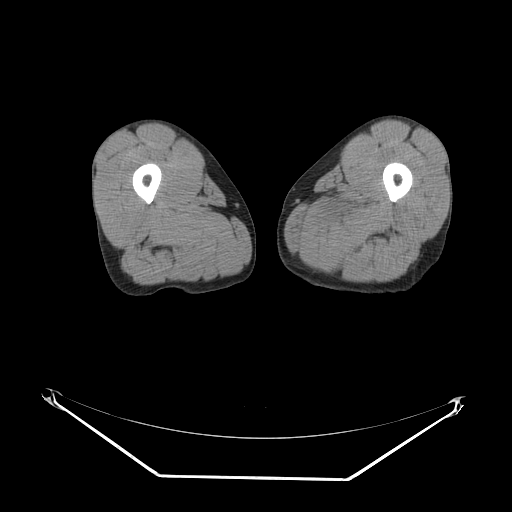
CT of an extremity soft-tissue mass (from a PET/CT study), one axial slice. Slice 9 of 267 in the series (ordered by position). Reconstruction kernel SOFT. Soft-tissue window (W 400 / L 40 HU). 512 × 512 image matrix, field of view 500 × 500 mm. Male patient. Case-level facts recorded for this patient, not image findings: histological type: pleiomorphic liposarcoma; grade: high; site of the primary tumour: left thigh.
Annotated regions visible in this slice (expert contour drawn on MRI and transferred to this co-registered scan by the dataset authors):
- gross tumour volume including surrounding oedema: bounding box [x1, y1, x2, y2] px = [326, 199, 369, 232]